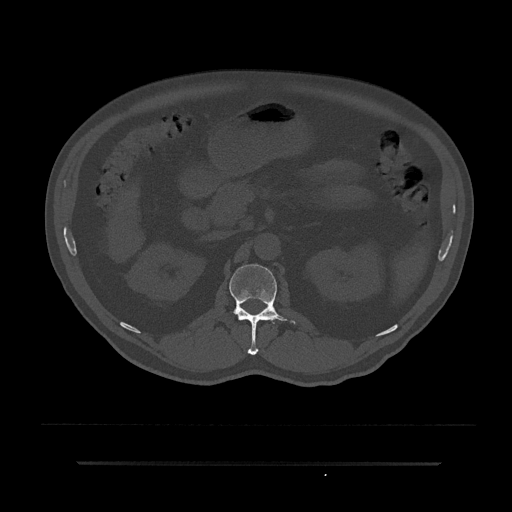
CT including the spine, one axial slice; slice 142 of 797 in the series (ordered by position); reconstruction kernel Br40s/3; 120 kVp; bone window (W 1800 / L 400 HU); 512 × 512 image matrix, field of view 464 × 464 mm. Patient: male, 59 years. From the clinical record (not read from this slice): primary cancer: bile ducts.
Structures marked on this image (semi-automatic segmentation, software-assisted and operator-edited):
- L1 vertebra: bounding box (x1, y1, x2, y2) in pixels: (229, 264, 296, 355)